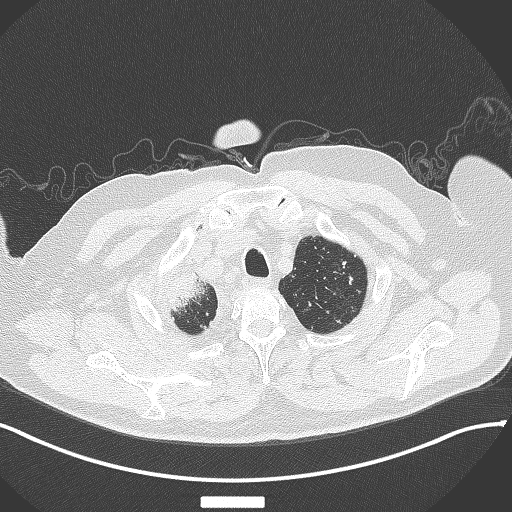
Chest CT, one axial slice; slice 330 of 384 in the series (ordered by position); reconstruction kernel B70f; 120 kVp; lung window (W 1500 / L -600 HU); 1 mm slice thickness; 512 × 512 image matrix, field of view 400 × 400 mm. Patient: male, 69 years. From the clinical record (not read from this slice): clinical TNM (as recorded): T4 N3 M1.
Structures marked on this image (rectangle marked by the reading radiologist):
- lung tumour (recorded histology: adenocarcinoma): box from (x=152, y=262) to (x=208, y=316) px